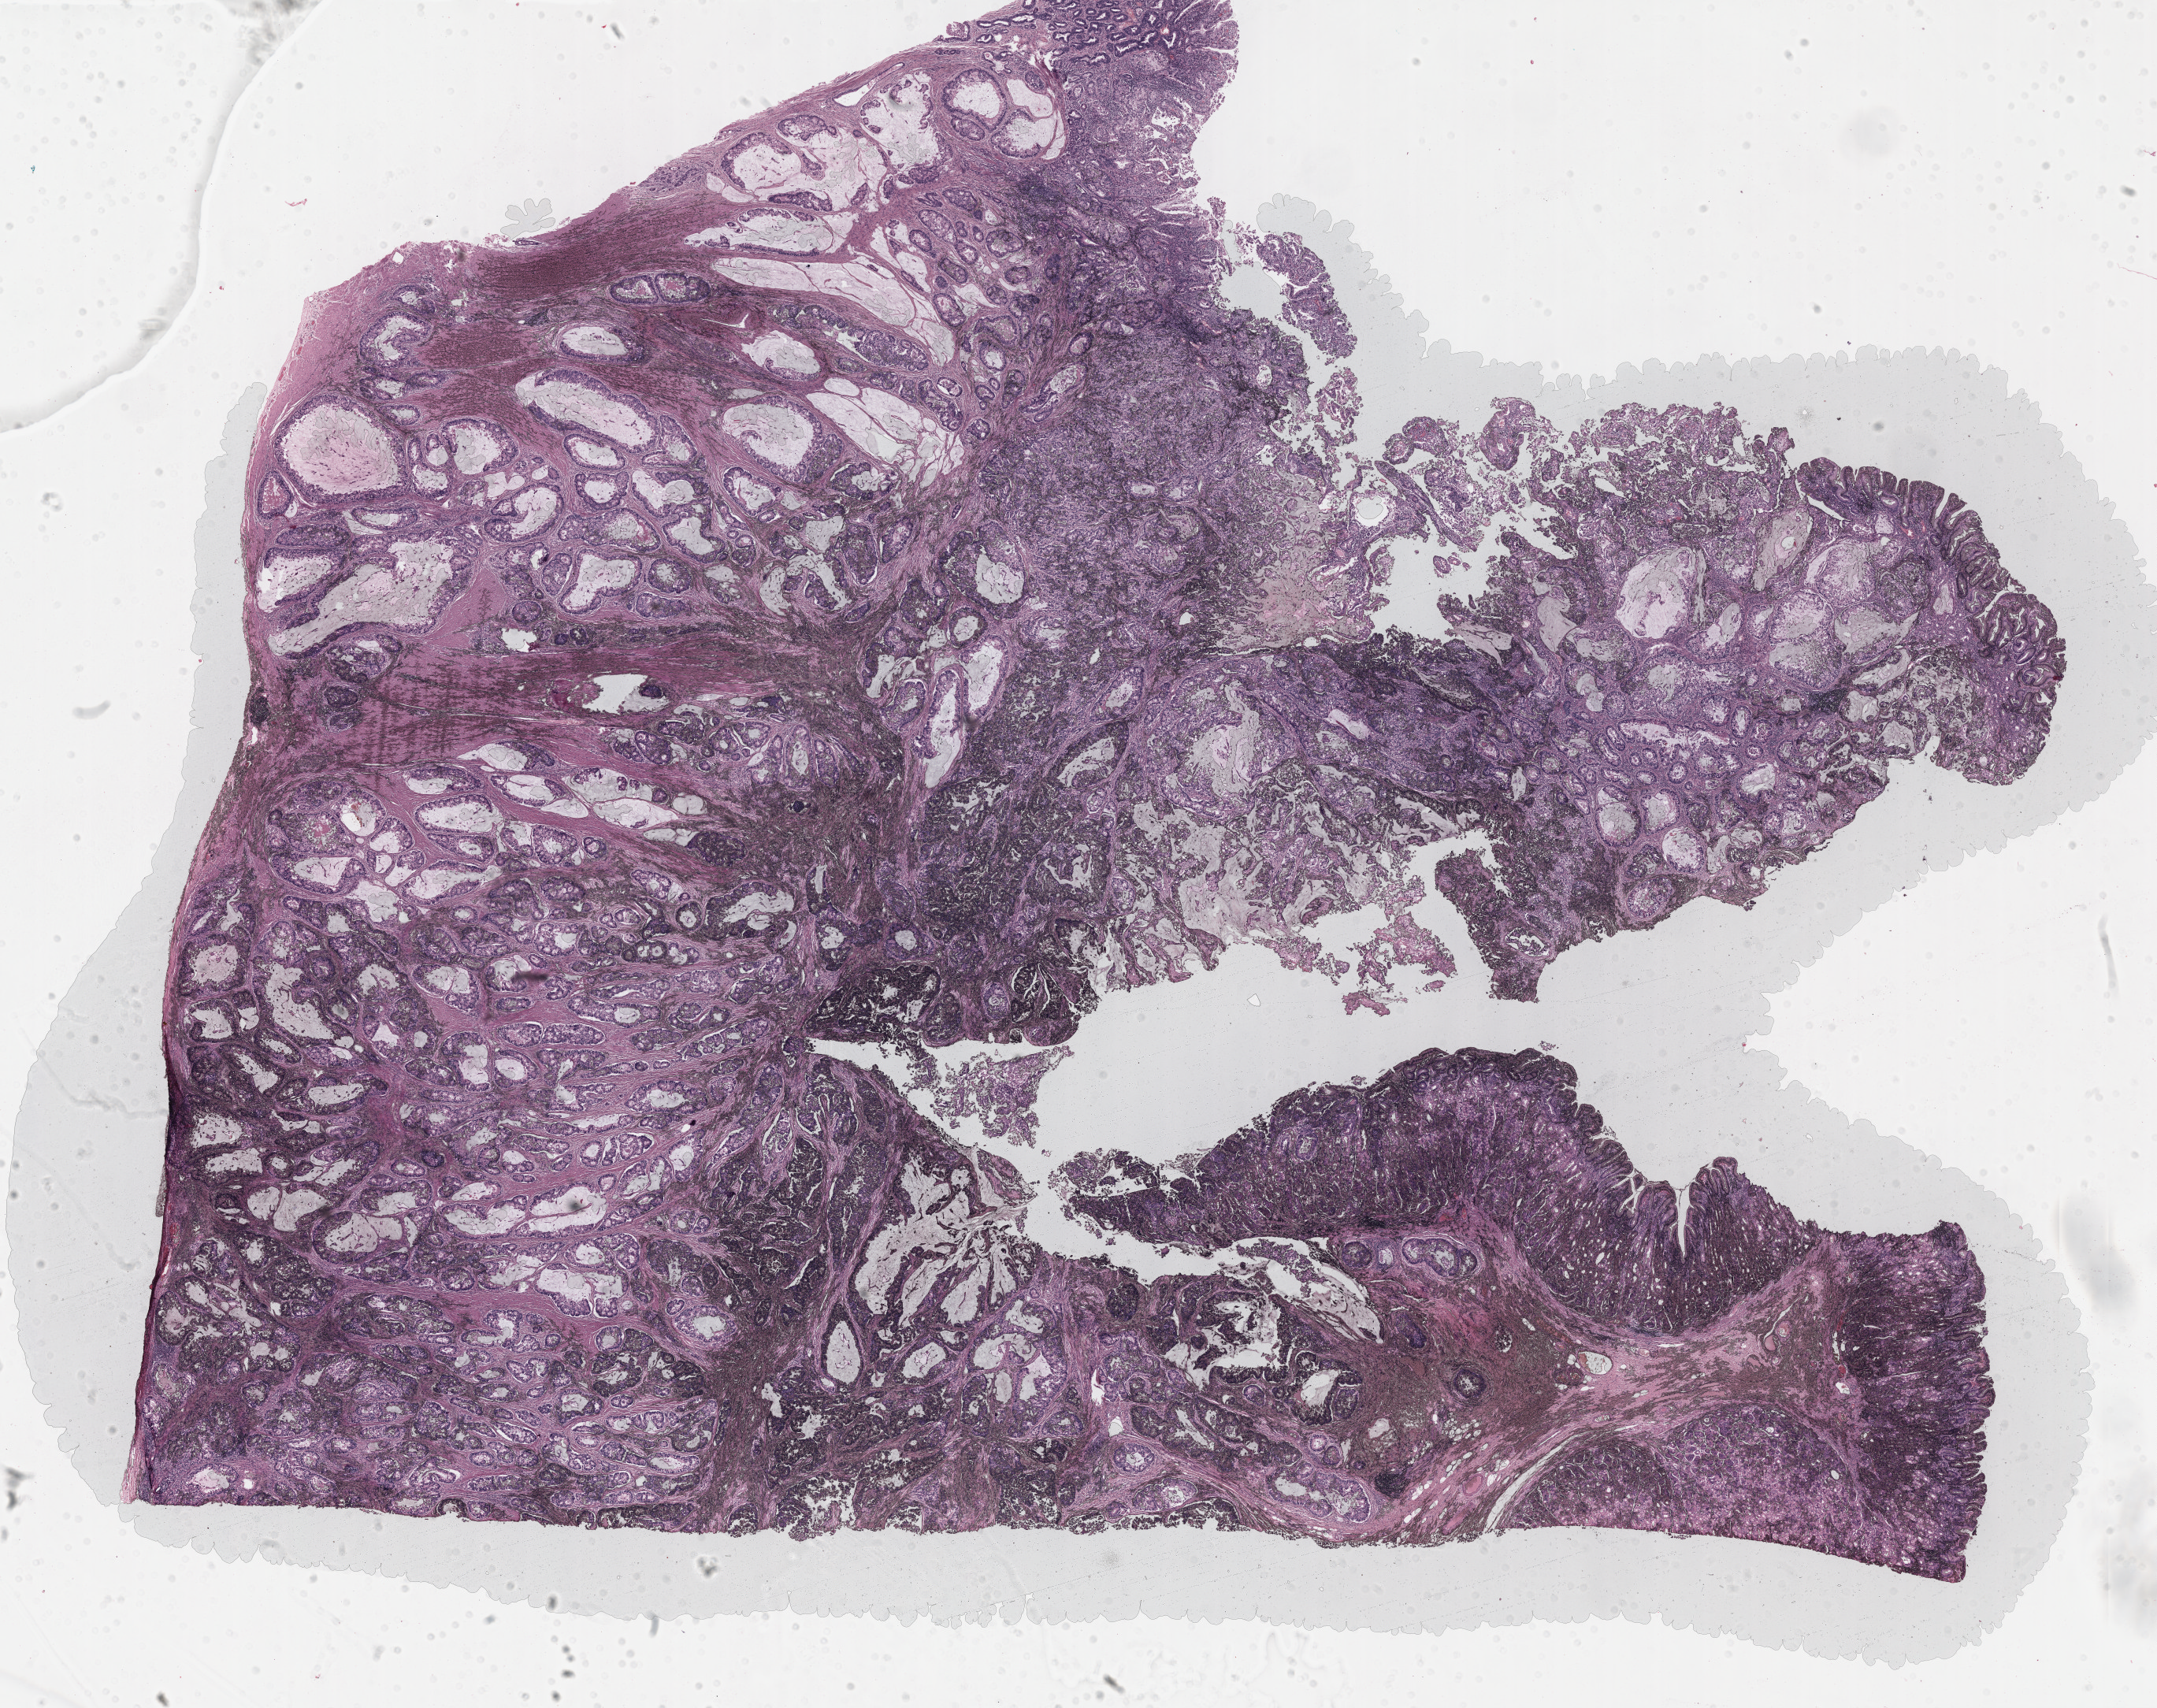
H&E-stained whole-slide image, shown as a low-resolution overview of the whole scanned area (about 22.1 x 17.5 mm, acquisition: 40x scan); formalin-fixed paraffin-embedded (FFPE) diagnostic section; sample: primary tumour, stomach. Patient: male, age at initial diagnosis 62 years. Histologic grade: G3 (poorly differentiated).
Lymph nodes positive (case pathology): 0 of 10 examined. TNM: T2 N0 M0. AJCC pathologic stage: IB (7th edition). Histologic diagnosis: Tubular adenocarcinoma (fundus of stomach).